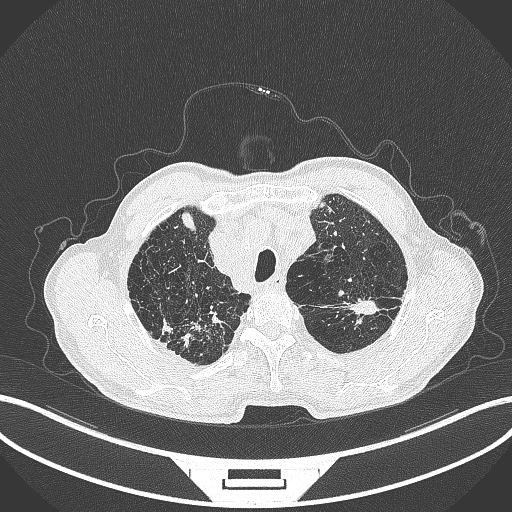
Chest CT, one axial slice. Position 376 of 463 along the scan axis. Reconstruction kernel B70f. Lung window (W 1500 / L -600 HU). 1 mm slice thickness. 512 × 512 image matrix. Male patient, age 74 years. Case-level facts recorded for this patient, not image findings: clinical TNM (as recorded): T2a N1 M0.
Structures marked on this image (rectangle marked by the reading radiologist):
- lung tumour (recorded histology: adenocarcinoma): bounding box [x1, y1, x2, y2] px = [340, 295, 380, 318]